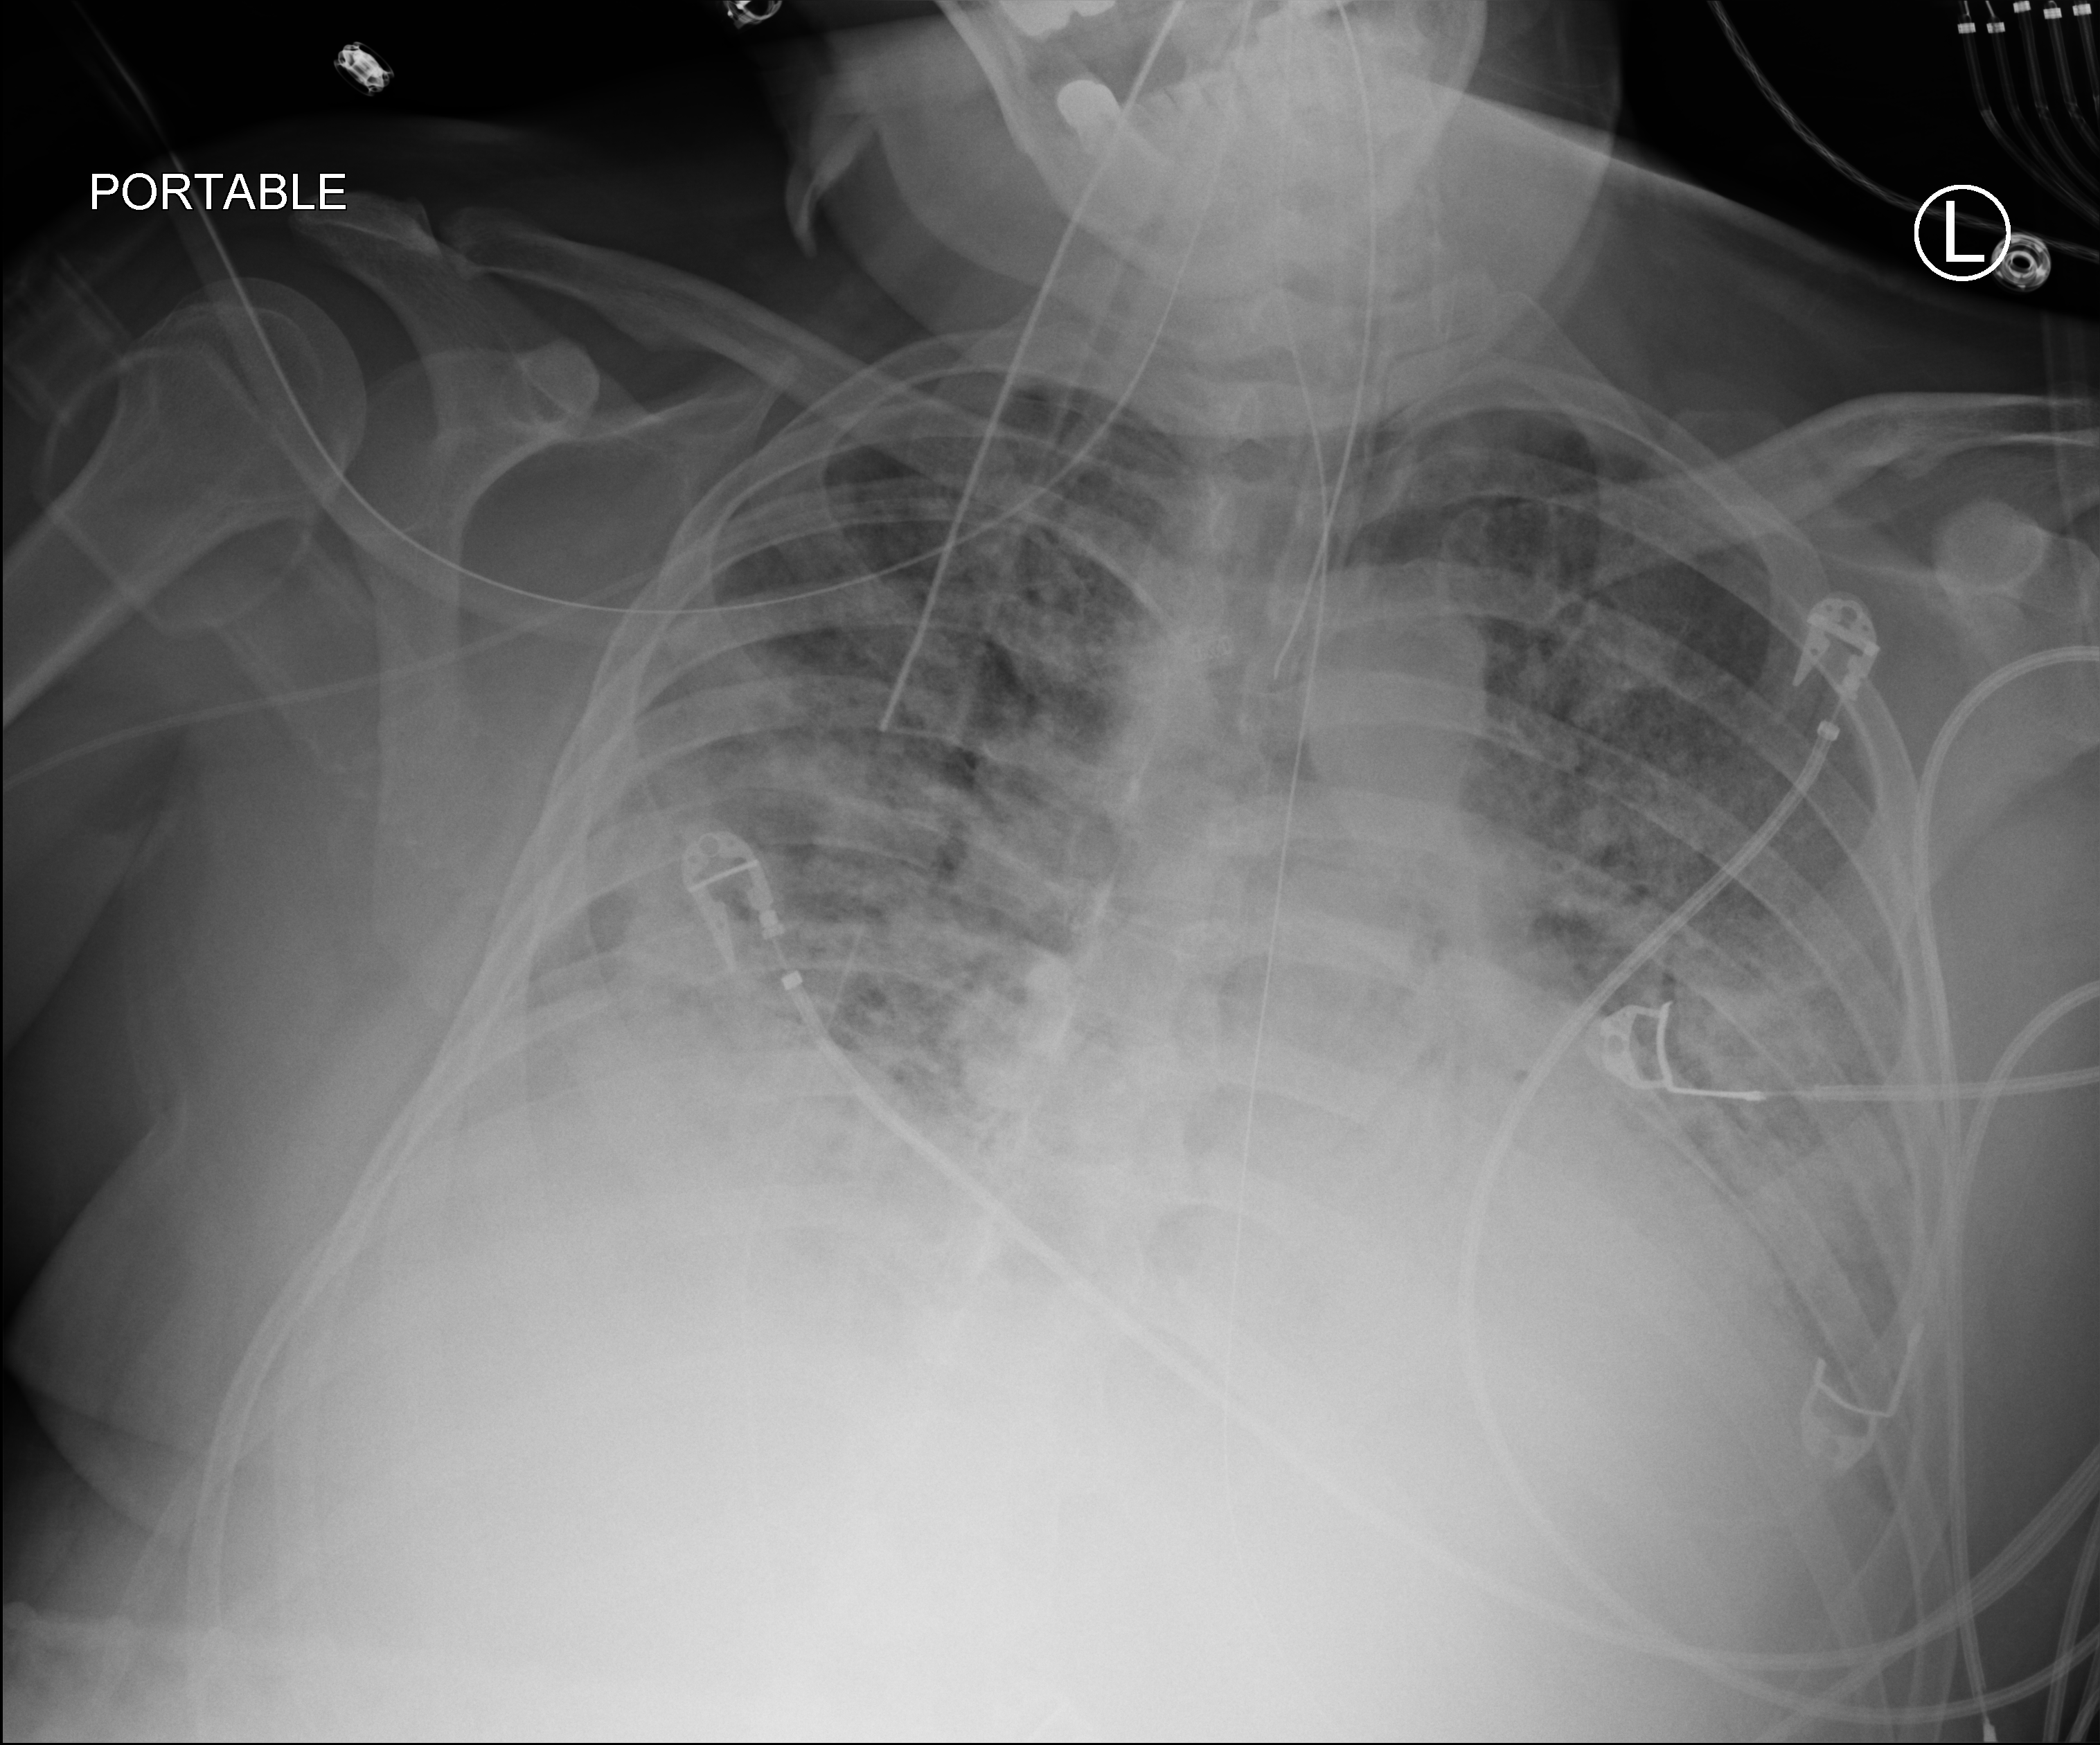
Bedside chest radiograph (computed radiography); anteroposterior (AP) projection. Patient hospitalised with COVID-19; male, aged 18–59 years.
Admission-level facts for this patient (not findings on this image; timing relative to this image not recorded): mechanically ventilated during this hospital stay: yes; admitted to intensive care during this hospital stay: yes.